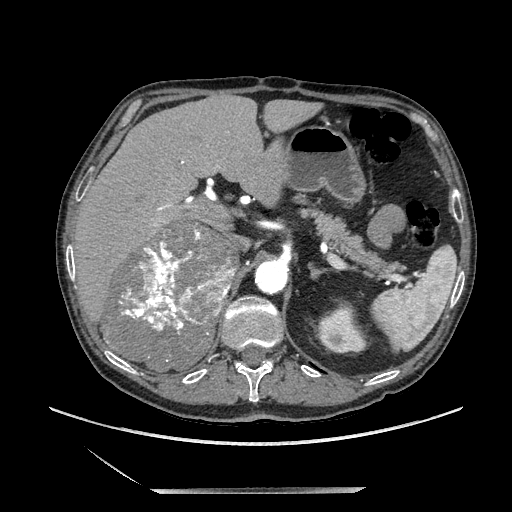
Contrast-enhanced abdominal CT, one axial slice. Position 141 of 243 along the scan axis. Soft-tissue window (W 400 / L 40 HU). 1.25 mm slice thickness. 512 × 512 image matrix, field of view 420 × 420 mm. Male patient. From the clinical record (not read from this slice): diagnosis: adrenocortical carcinoma; tumour side: right adrenal; tumour size at pathology: 16 cm; Ki-67 index: 17 %; stage (as recorded): 3.
Outlined on this slice (semi-automatically segmented with operator editing):
- mass: box from (x=103, y=221) to (x=236, y=370) px